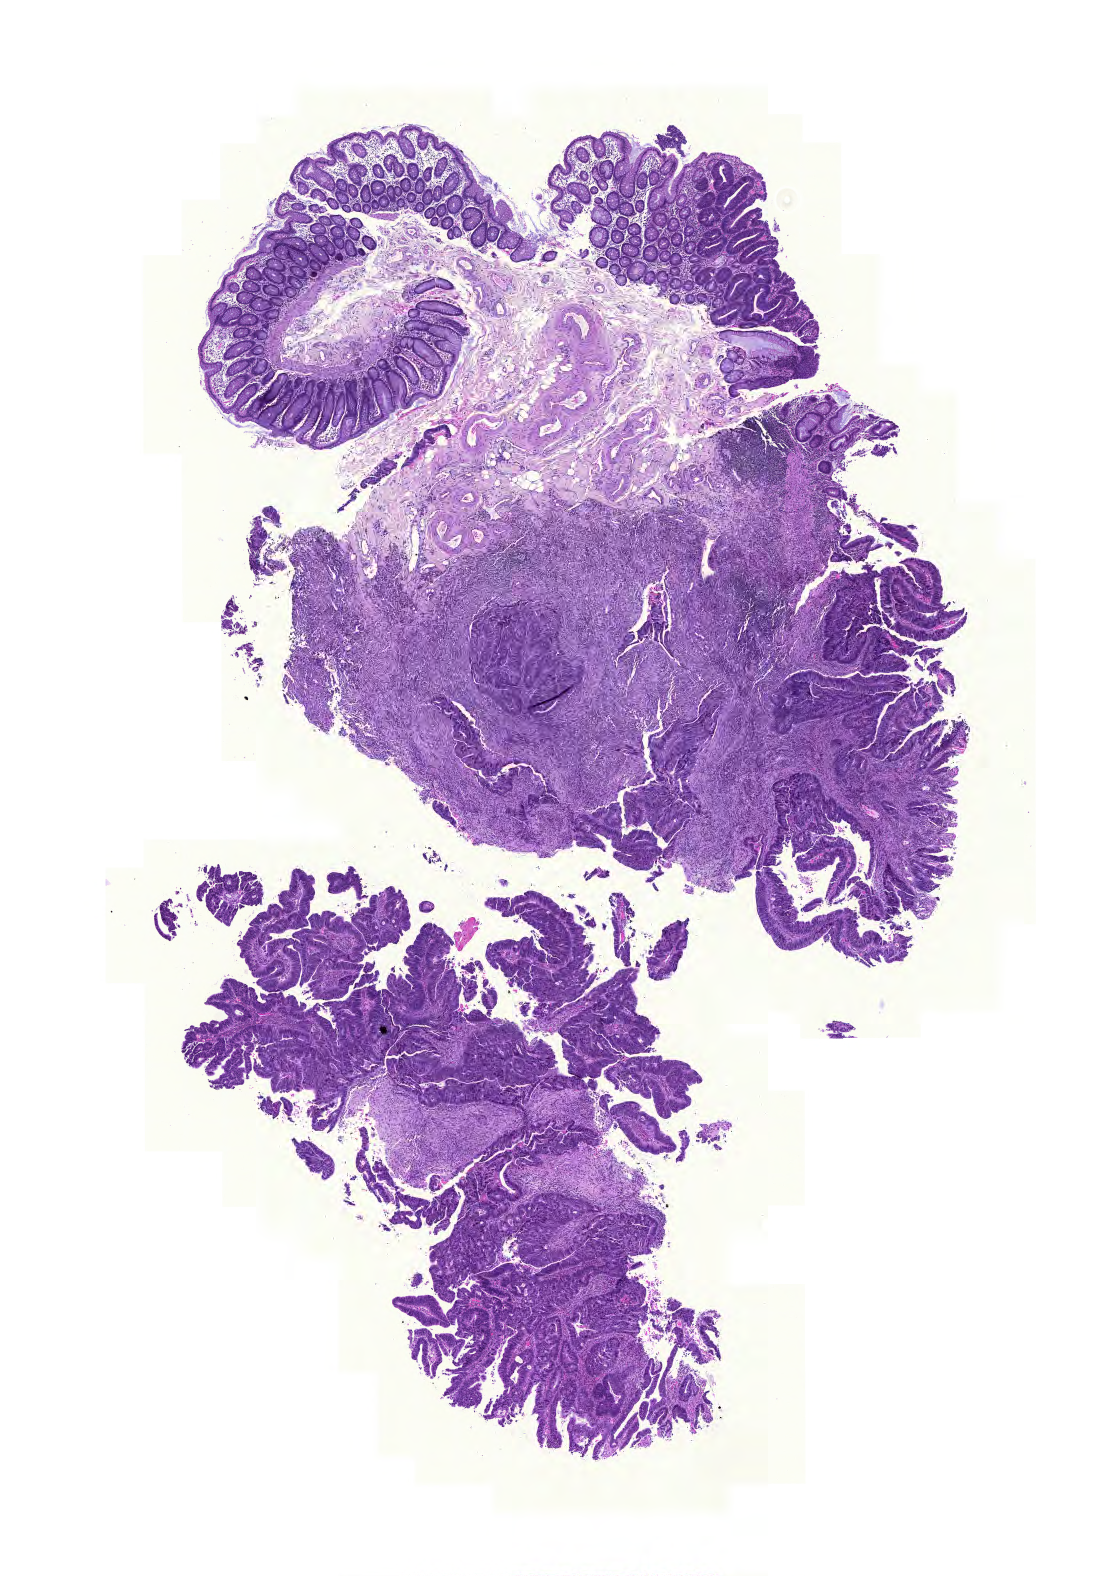
Whole-slide histology image, H&E-stained, a low-resolution overview of the entire scanned area, about 8.3 x 11.7 mm (from a 20x scan); formalin-fixed paraffin-embedded (FFPE) diagnostic section; primary tumour sample from the colon. Female, age 78 years at initial diagnosis.
Pathologic diagnosis: Adenocarcinoma, NOS. Lymph nodes positive (case pathology): 0 of 31 examined. AJCC pathologic stage: I (6th edition). TNM: T1 N0 M0.